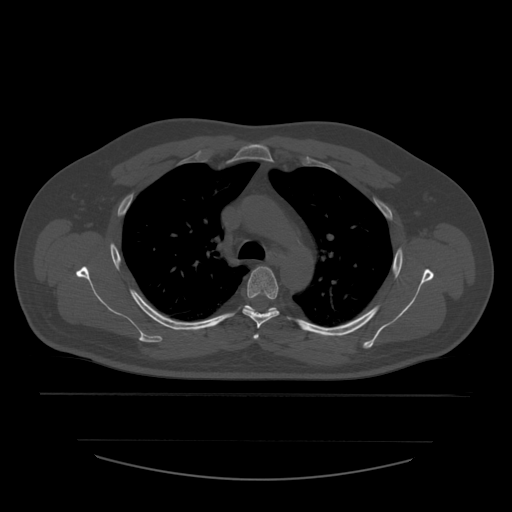
CT including the spine, one axial slice. Position 414 of 532 along the scan axis. Bone window (W 1800 / L 400 HU). 1.25 mm slice thickness. 512 × 512 image matrix. Patient age 44 years. From the clinical record (not read from this slice): primary cancer: soft tissue sarcoma.
Outlined on this slice (semi-automatic segmentation, software-assisted and operator-edited):
- T3 vertebra: bounding box [x1, y1, x2, y2] px = [253, 334, 259, 340]
- T4 vertebra: [243, 267, 280, 329]
- T5 vertebra: [246, 305, 277, 314]